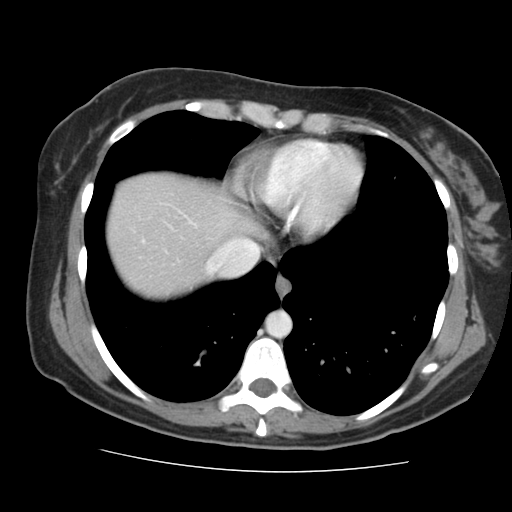
Contrast-enhanced abdominal CT, one axial slice; slice 135 of 144 in the series (ordered by position); intravenous contrast given; soft-tissue window (W 400 / L 40 HU); 512 × 512 image matrix, field of view 333 × 333 mm. Female patient, age 46 years. Case-level facts recorded for this patient, not image findings: diagnosis: colorectal cancer liver metastases, imaged before liver resection; multiple liver metastases: no; largest metastasis: 2.8 cm; disease in both lobes: no.
Annotated regions visible in this slice (outlined manually by an expert reader):
- hepatic veins: bounding box (x1, y1, x2, y2) in pixels: (207, 239, 259, 274)
- liver: (108, 175, 254, 297)
- planned liver remnant (the part of the liver to remain after resection): (108, 175, 254, 297)